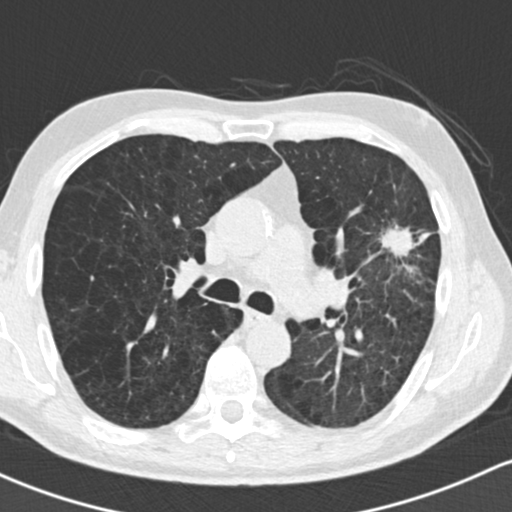
Low-dose screening chest CT, axial slice. Baseline annual screen. Lung window (W 1500 / L -600 HU). 2 mm slice thickness. Standard (soft-tissue) reconstruction kernel (B30f). 120 kVp. Slice 67 of 162 in the series. Male participant, aged 61 years at enrolment.
• Expert reader's lesion annotation, bounding box <357,187,458,296> (left, top, right, bottom; pixels).
• Reader record for this screening exam (exam-level; its link to the box is not recorded): non-calcified nodule or mass ≥4 mm, left upper lobe, 35 × 35 mm, spiculated (stellate) margins, soft tissue attenuation.
• Participant outcome: lung cancer diagnosed 19 days after this screen — adenocarcinoma, NOS, left upper lobe, well differentiated (G1), stage IIIA (AJCC 6th edition), 45 mm at pathology.